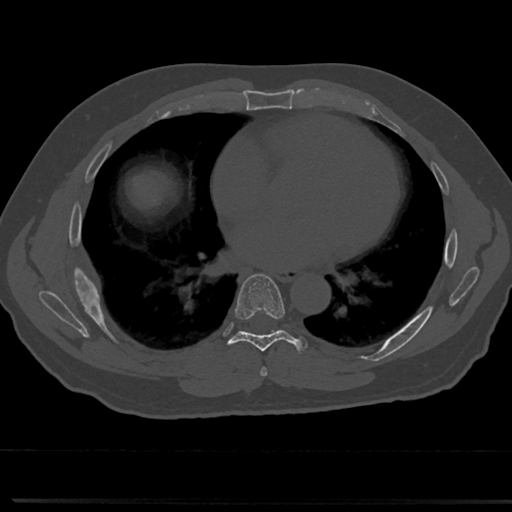
CT including the spine, one axial slice. Slice 403 of 817 in the series (ordered by position). Reconstruction kernel Br40s/3. 120 kVp. Bone window (W 1800 / L 400 HU). 0.5 mm slice thickness. 512 × 512 image matrix, field of view 355 × 355 mm. Patient: male, 61 years. From the clinical record (not read from this slice): primary cancer: prostate.
Outlined on this slice (semi-automatic segmentation, software-assisted and operator-edited):
- T6 vertebra: bounding box <260,340,319,375> (left, top, right, bottom; pixels)
- T7 vertebra: <214,275,309,358>